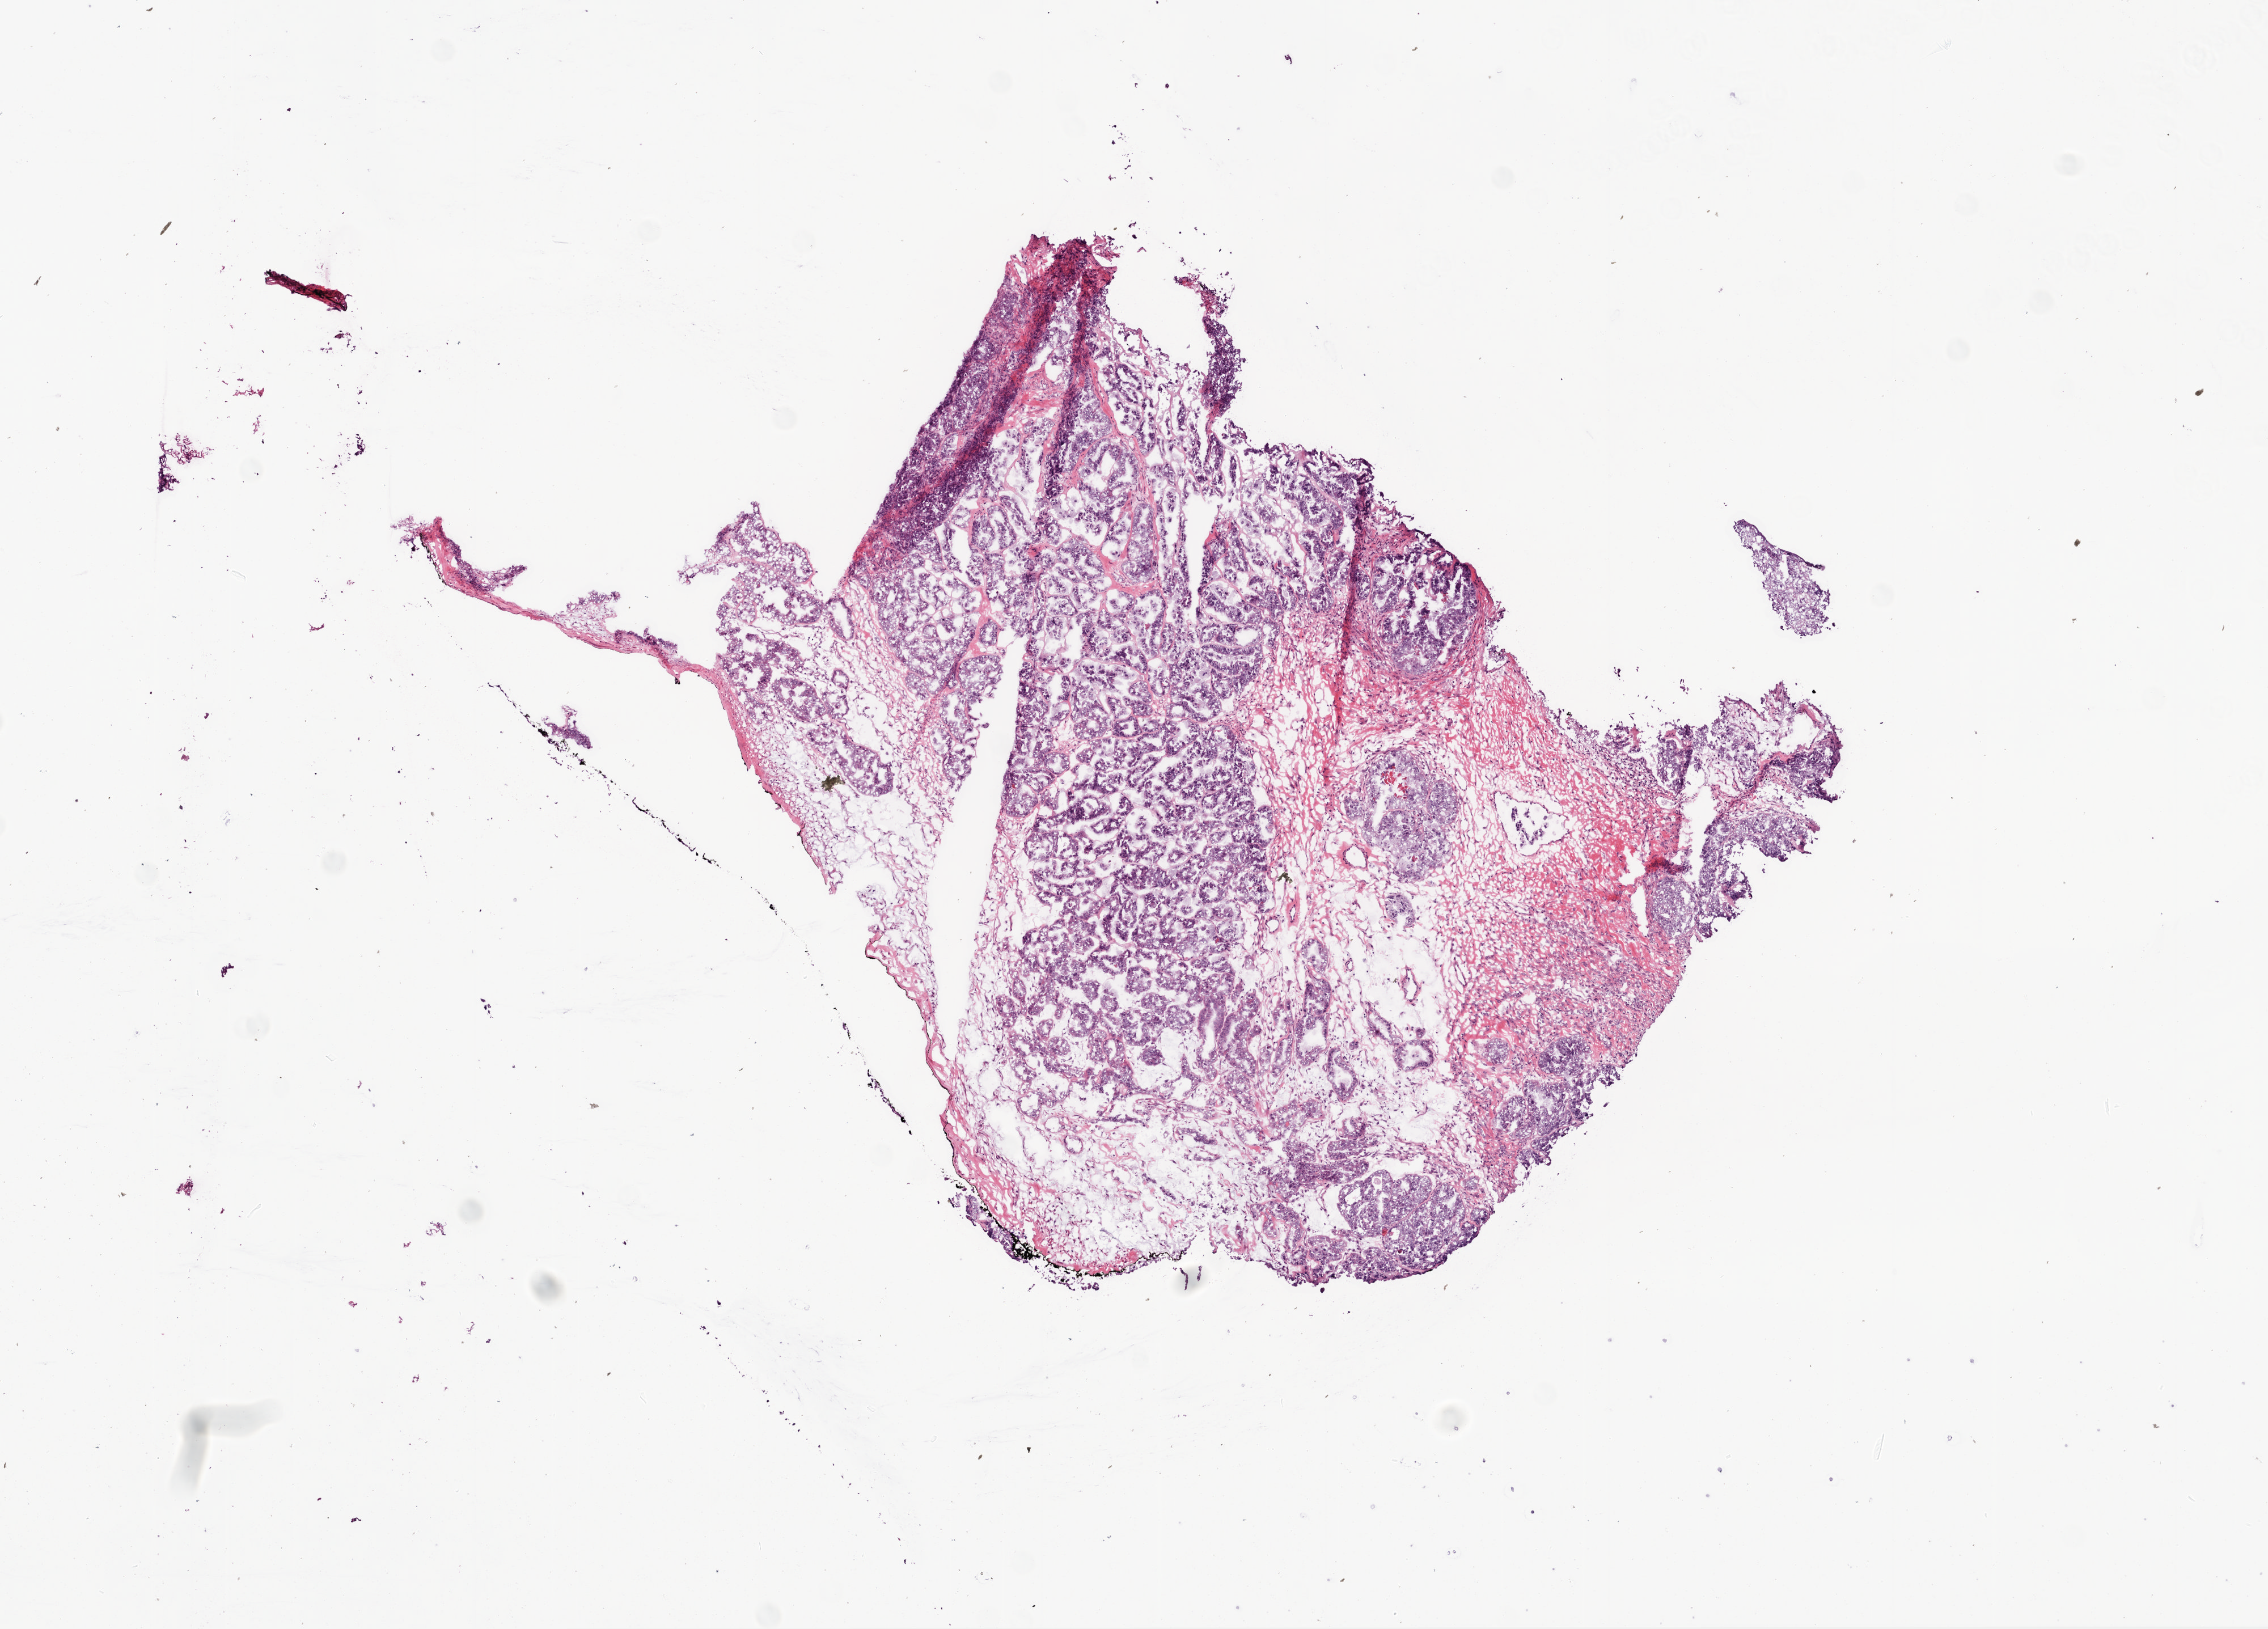
Hematoxylin and eosin (H&E) stained whole-slide image, whole scanned area (about 8.0 x 5.8 mm, acquisition: 20x scan) shown as a low-resolution overview; frozen section; ovary, primary tumour sample. Female patient; age at initial diagnosis 75 years. Histologic grade: G3 (poorly differentiated). Composition of this section per pathologist review: tumour cells 70%, tumour nuclei 80%, normal cells 28%, stromal cells 0%, necrosis 2%.
FIGO stage: IIIC. Histologic diagnosis: Serous cystadenocarcinoma, NOS.